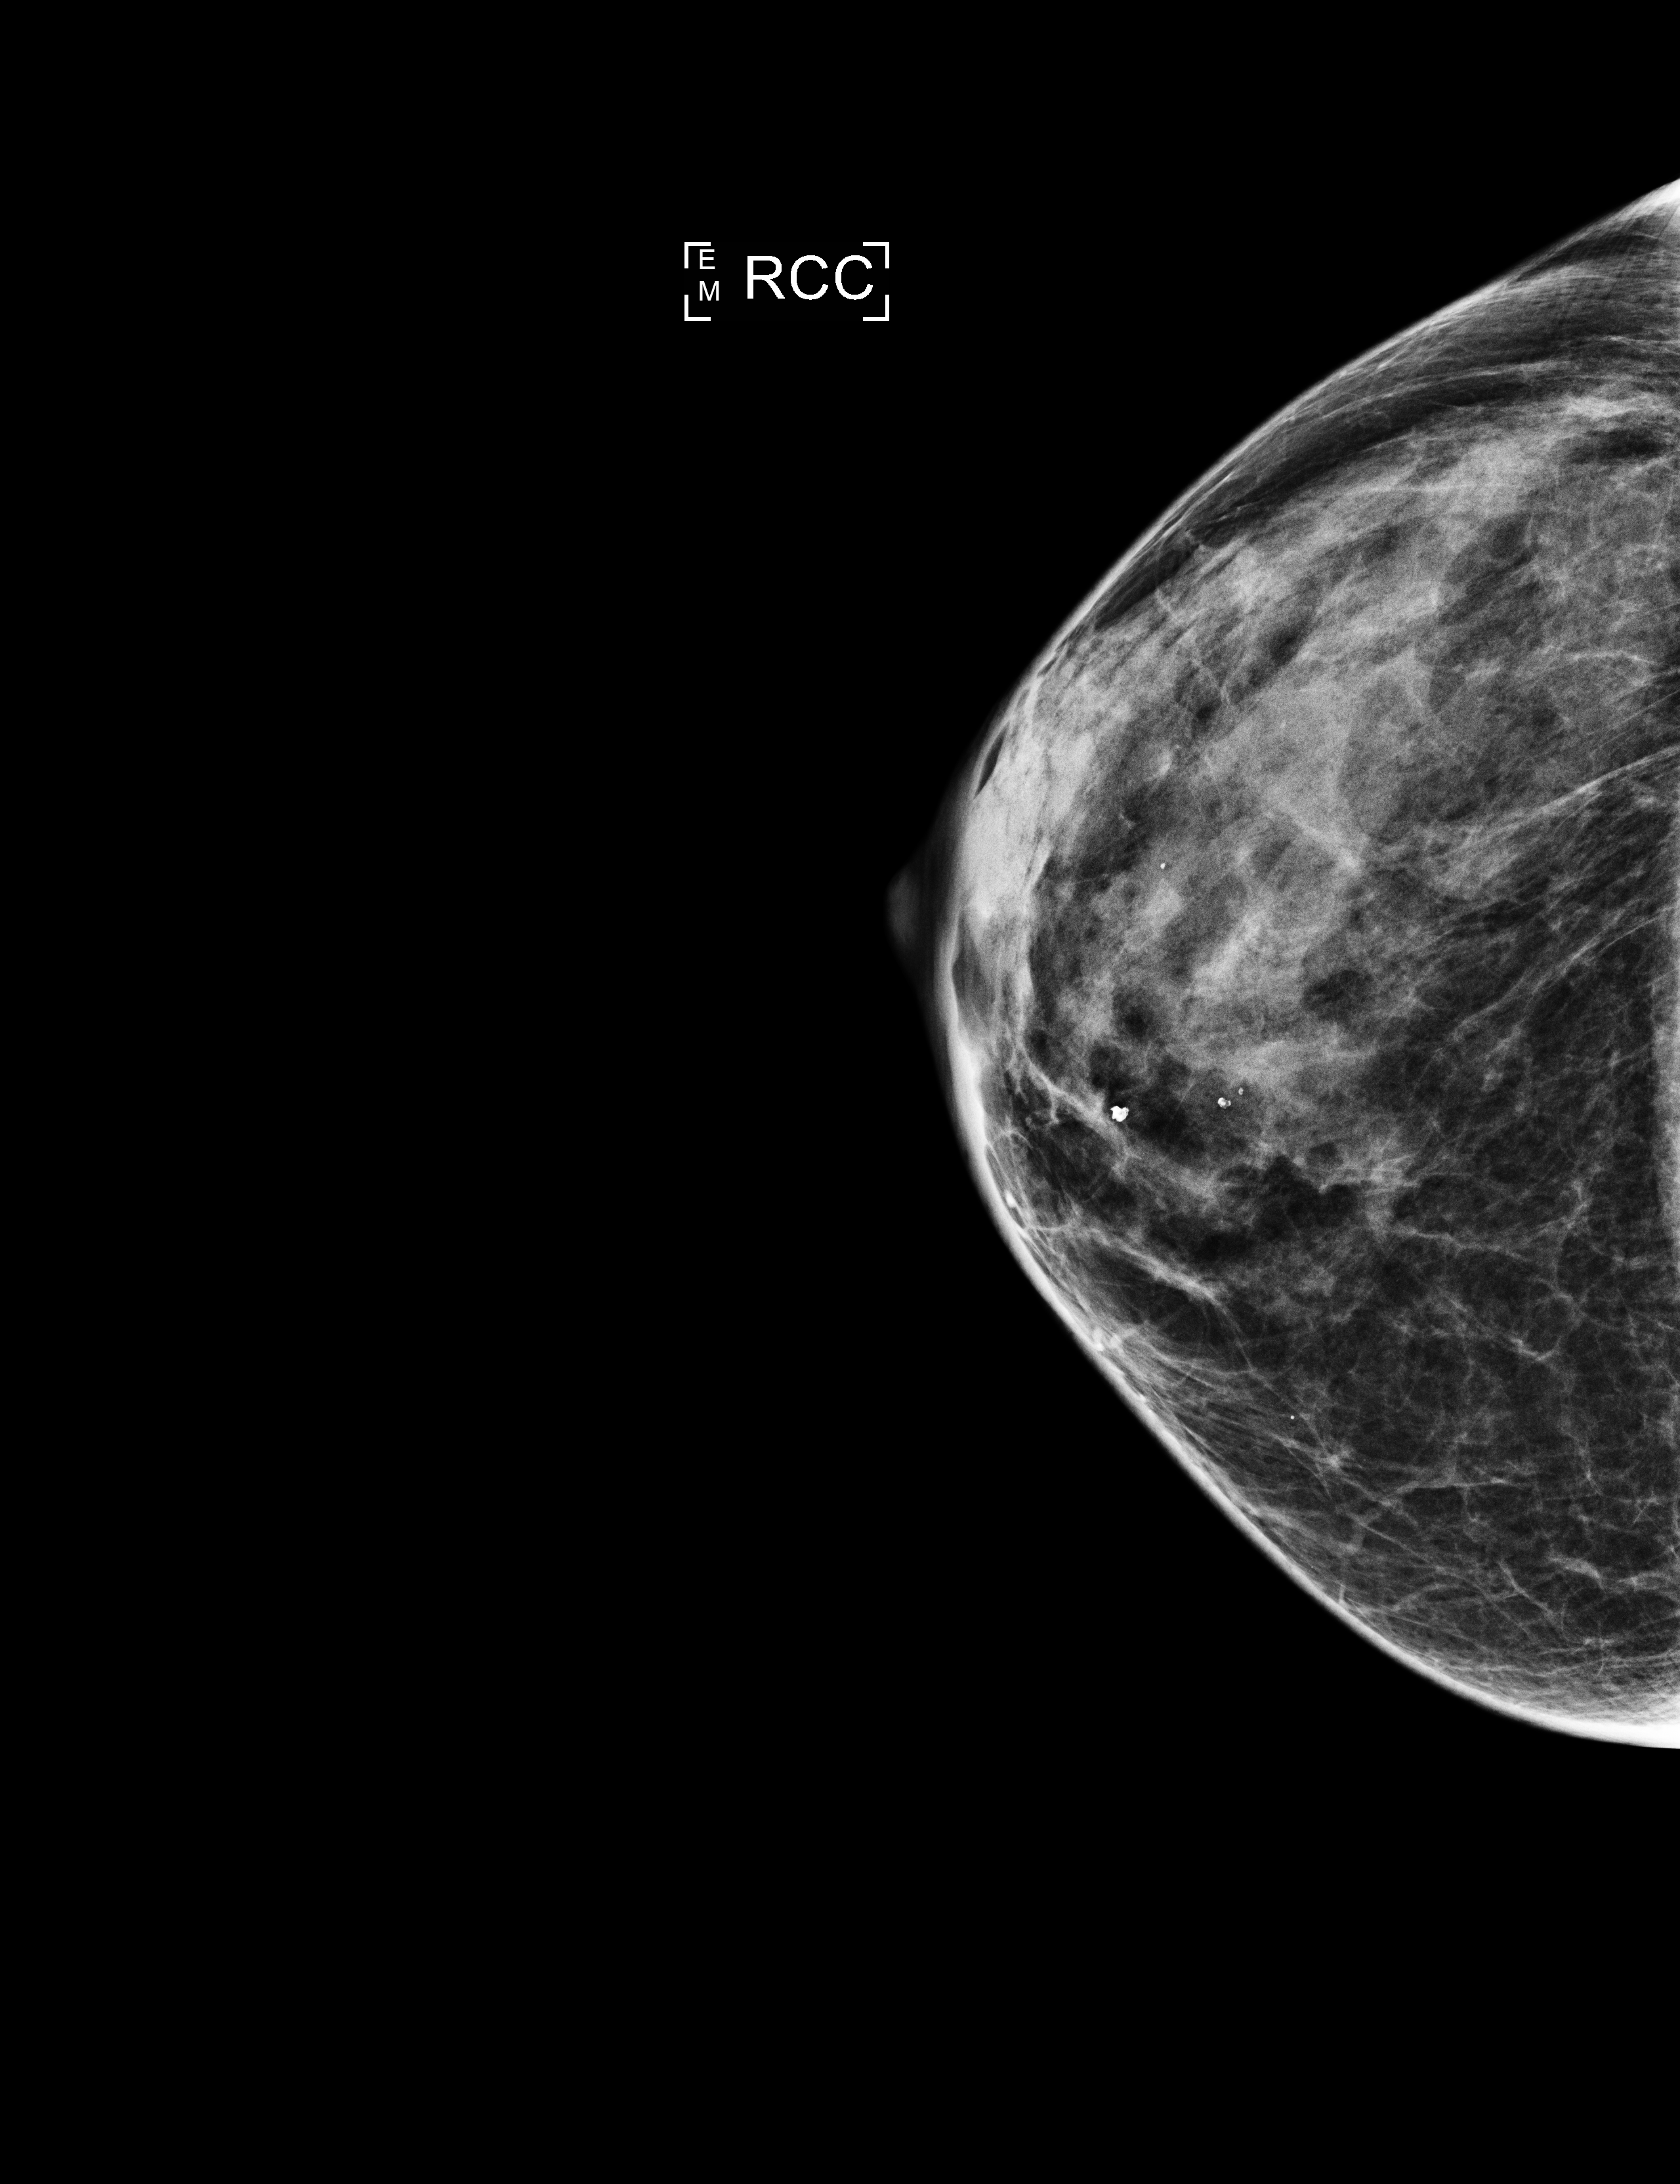
Digital mammogram (FFDM); right breast; cranio-caudal projection; annual screening mammography examination; compressed breast thickness 39 mm. Patient: female, 65 years.
Breast density at the screening exam (both breasts): extremely dense (BI-RADS density category d). Final BI-RADS assessment for this screening round (tomosynthesis exam, both breasts): category 2. Recall: recalled for additional imaging after this screen.